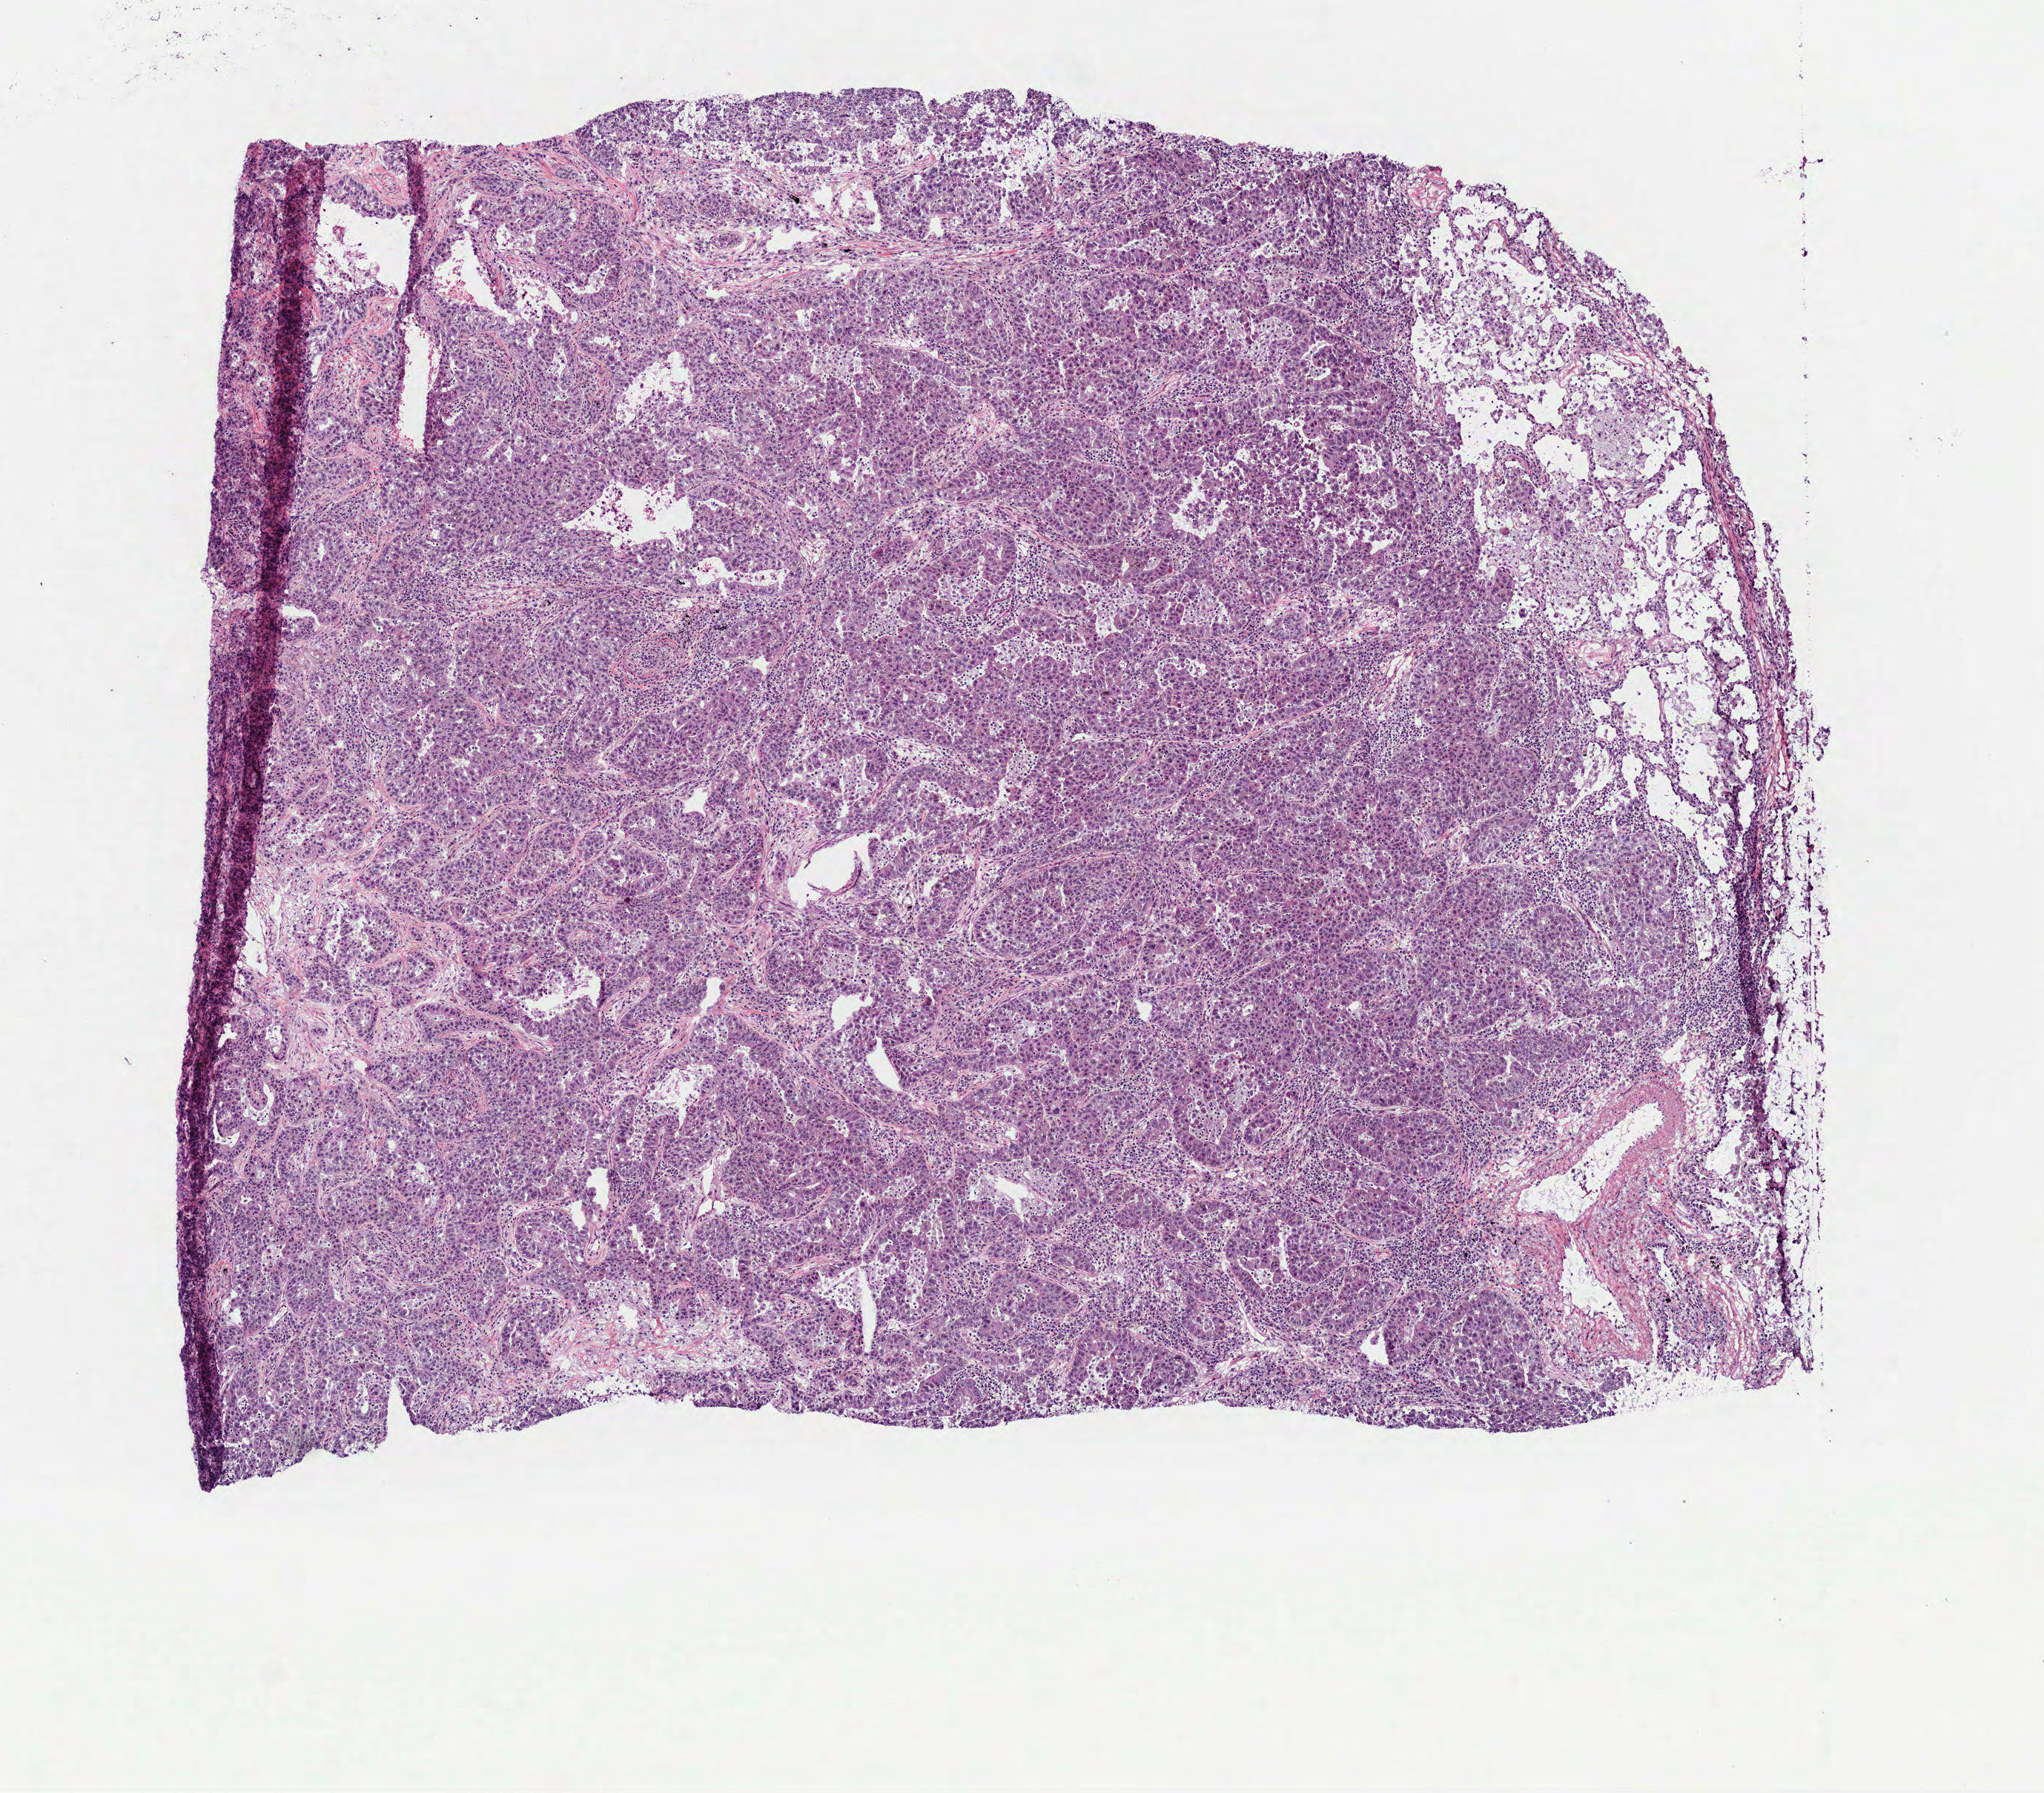
Whole-slide histology image, H&E-stained — shown as a low-resolution overview of the whole scanned area (about 5.6 x 4.9 mm, from a 40x scan); frozen section; primary tumour sample from the lung. Female patient. Slide review estimates, as recorded: tumour cells 75%, tumour nuclei 62%, normal cells 8%, stromal cells 15%, necrosis 2%. Infiltration values recorded for this section: lymphocyte infiltration 25%, monocyte infiltration 8%, neutrophil infiltration 0%.
Histologic diagnosis: Adenocarcinoma, NOS (upper lobe, lung). Laterality: right. TNM: T2 N0 M0. AJCC pathologic stage: IB (6th edition).